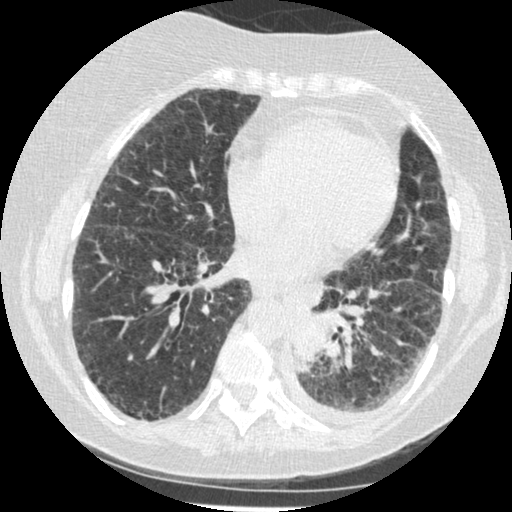
Low-dose screening chest CT, axial slice. Third screening round (two years after baseline). Lung window (W 1500 / L -600 HU). Slice 257 of 341 in the series. Female, age 60 years at enrolment.
Expert reader's lesion annotation, bounding box (x1, y1, x2, y2) in pixels: (278, 302, 343, 377). Screening reader's record for this exam (one nodule recorded; not confirmed to be the boxed lesion): non-calcified nodule or mass ≥4 mm, left lower lobe, 54 × 38 mm, smooth margins, soft tissue attenuation, pre-existing on the prior screen: yes; interval growth: yes. Official screen result: positive, other. Participant outcome: lung cancer diagnosed 15 days after this screen — small cell carcinoma, NOS, left lower lobe, undifferentiated (G4), stage IV (AJCC 6th edition), 69 mm at pathology.